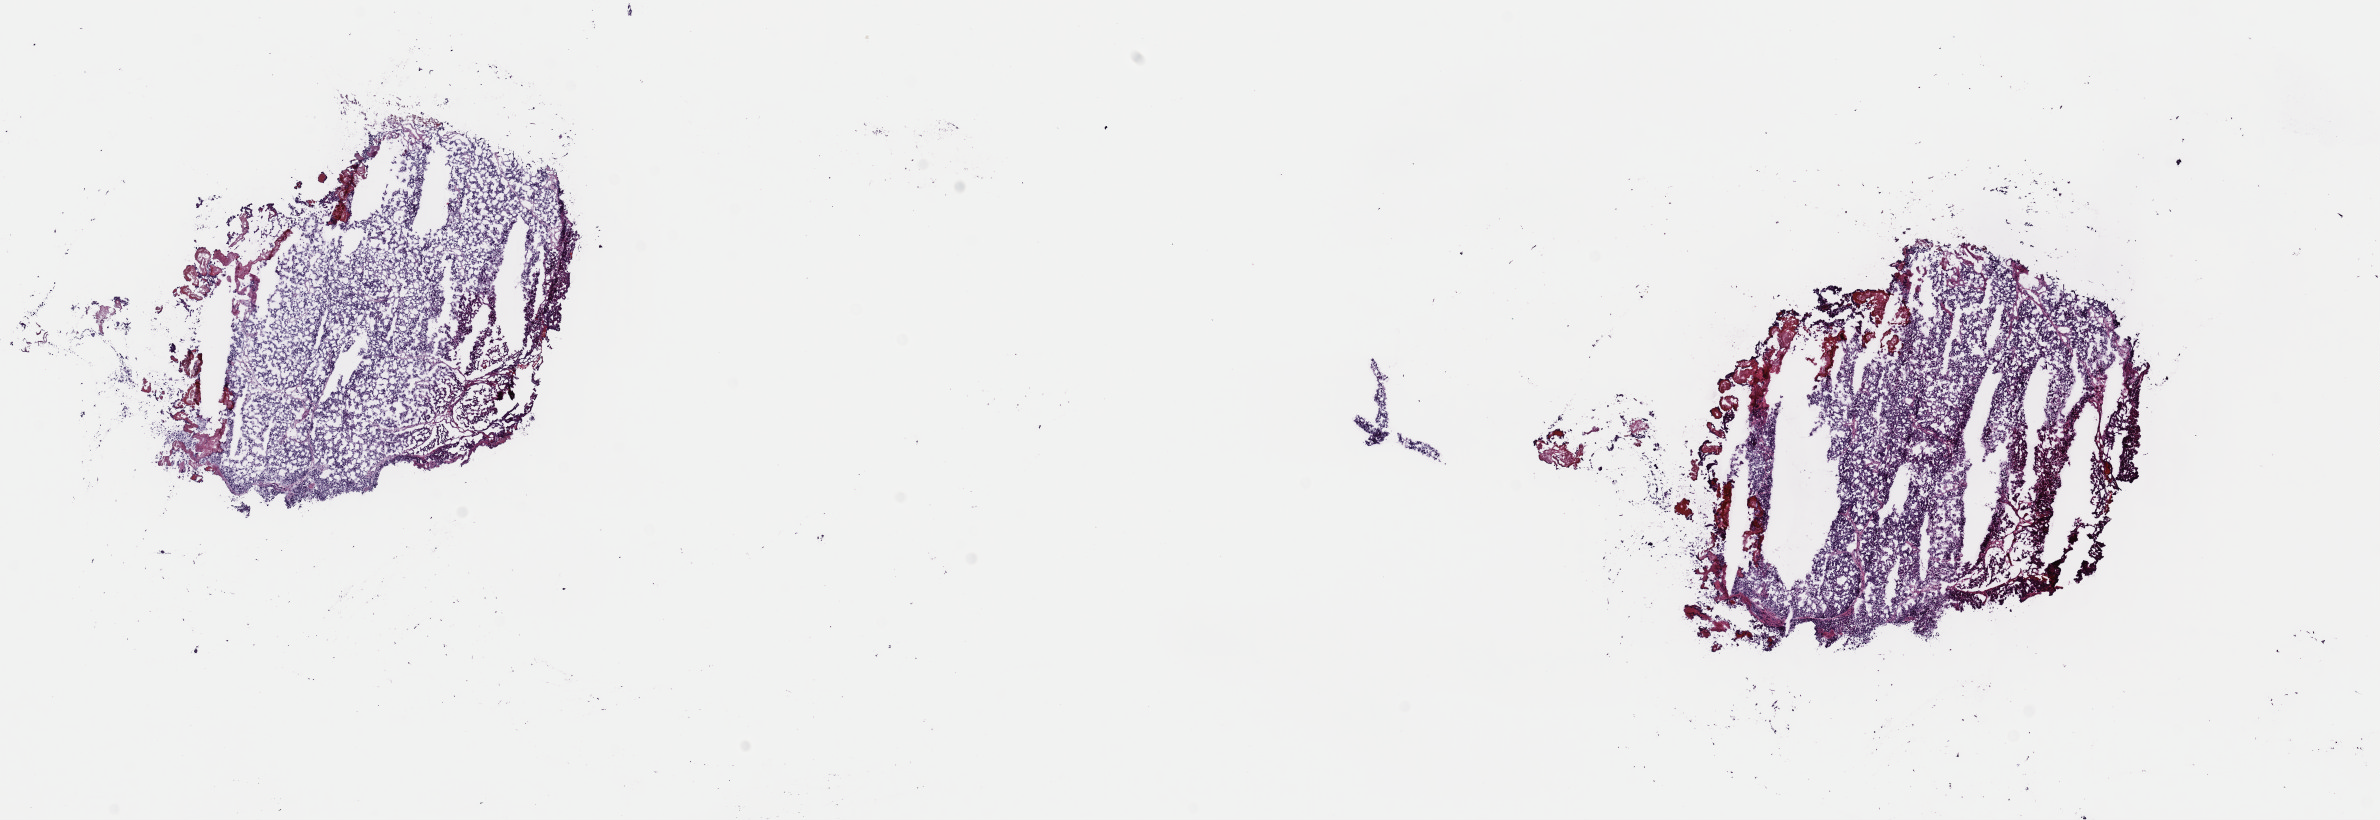
Whole-slide histology image, H&E — whole scanned area (about 18.8 x 6.5 mm, from a 40x scan) shown as a low-resolution overview, frozen section from the top of the tissue portion, sample: primary tumour, bladder. Male, age 72 years at initial diagnosis. Histologic grade: high grade. Composition of this section per pathologist review: tumour cells 90%, tumour nuclei 90%, normal cells 5%, stromal cells 5%, necrosis 0%. Infiltration values recorded for this section: lymphocyte infiltration 0%, monocyte infiltration 0%, neutrophil infiltration 0%.
Diagnosis: Transitional cell carcinoma. Lymph nodes positive (case pathology): 0 of 27 examined. AJCC pathologic stage: II (7th edition).